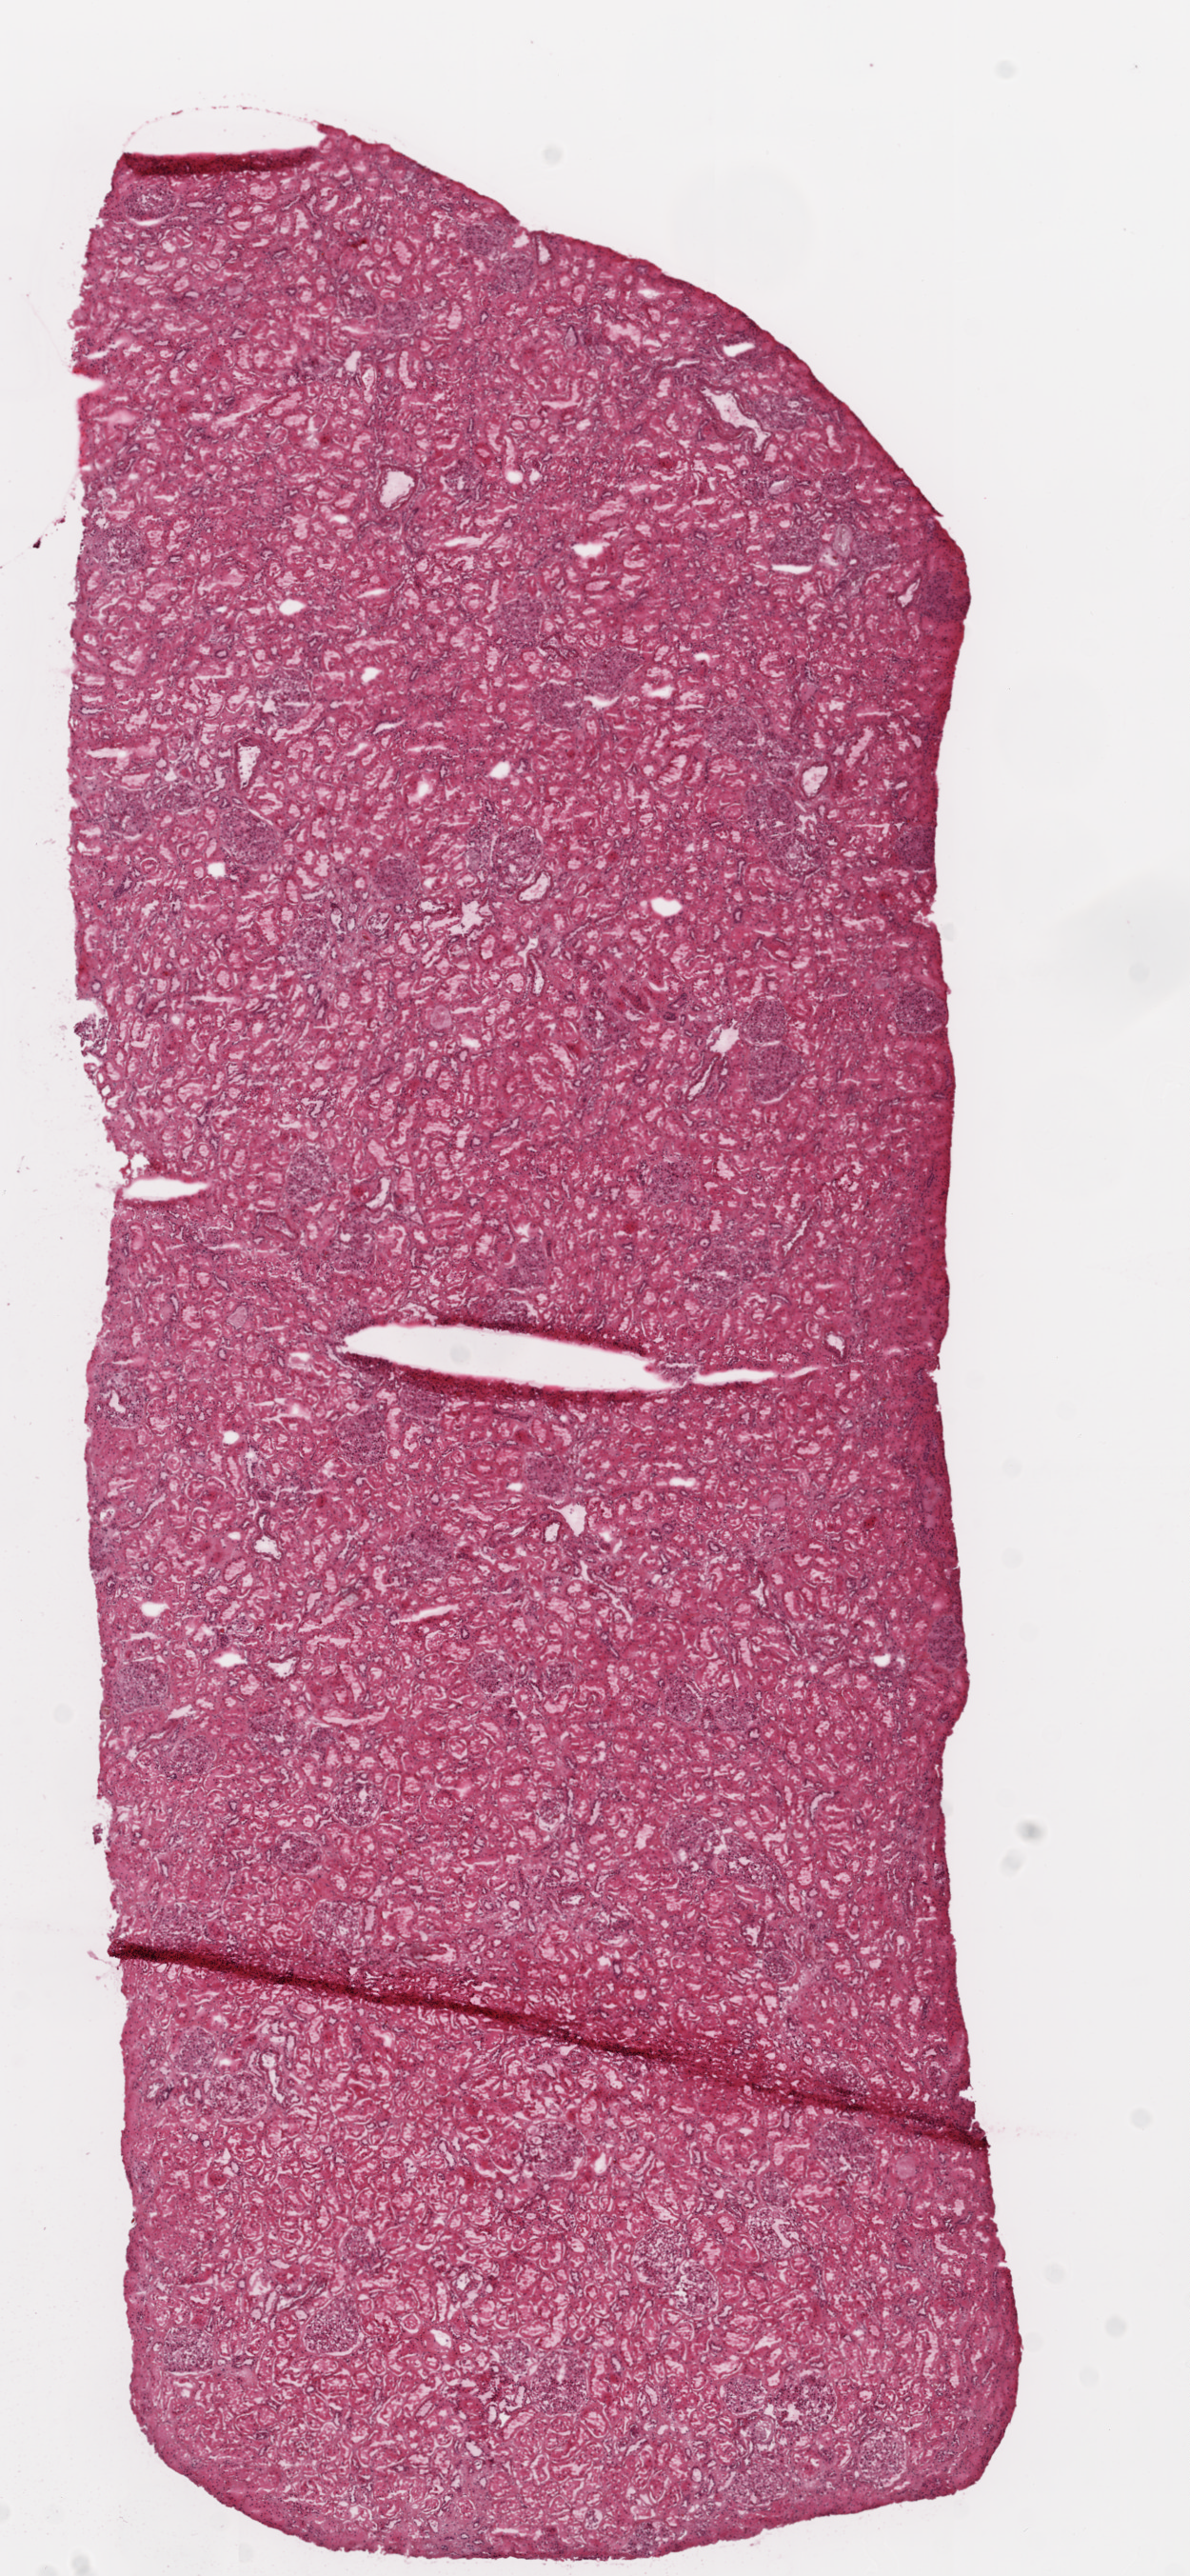
Digitized Hematoxylin and eosin (H&E) stained tissue section (whole slide) — a low-resolution overview of the entire scanned area, about 5.0 x 10.9 mm (from a 20x scan); frozen section from the top of the tissue portion; sample: solid tissue normal (non-tumour tissue), kidney. Female, age 63 years at initial diagnosis.
This section: solid tissue normal sample (biorepository sample class). Patient diagnosis: Clear cell adenocarcinoma, NOS.